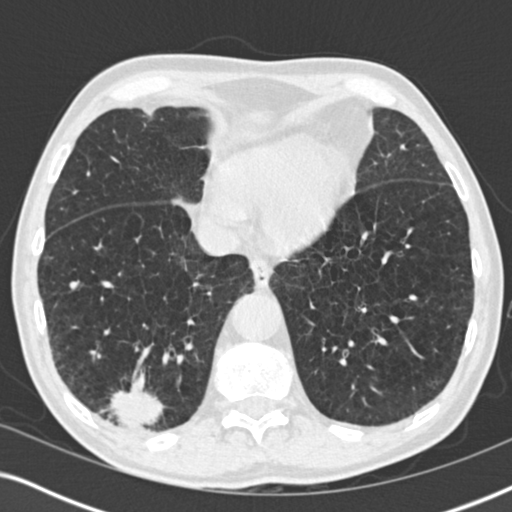
Low-dose screening chest CT, one axial slice. Slice 60 of 196 in the series (ordered by position). Reconstruction kernel B30f. Lung window (W 1500 / L -600 HU). 512 × 512 image matrix.
Annotated regions visible in this slice (outlined manually by an expert reader):
- lesion 3 (tumor, lower lobe of right lung): box from (x=109, y=382) to (x=162, y=429) px